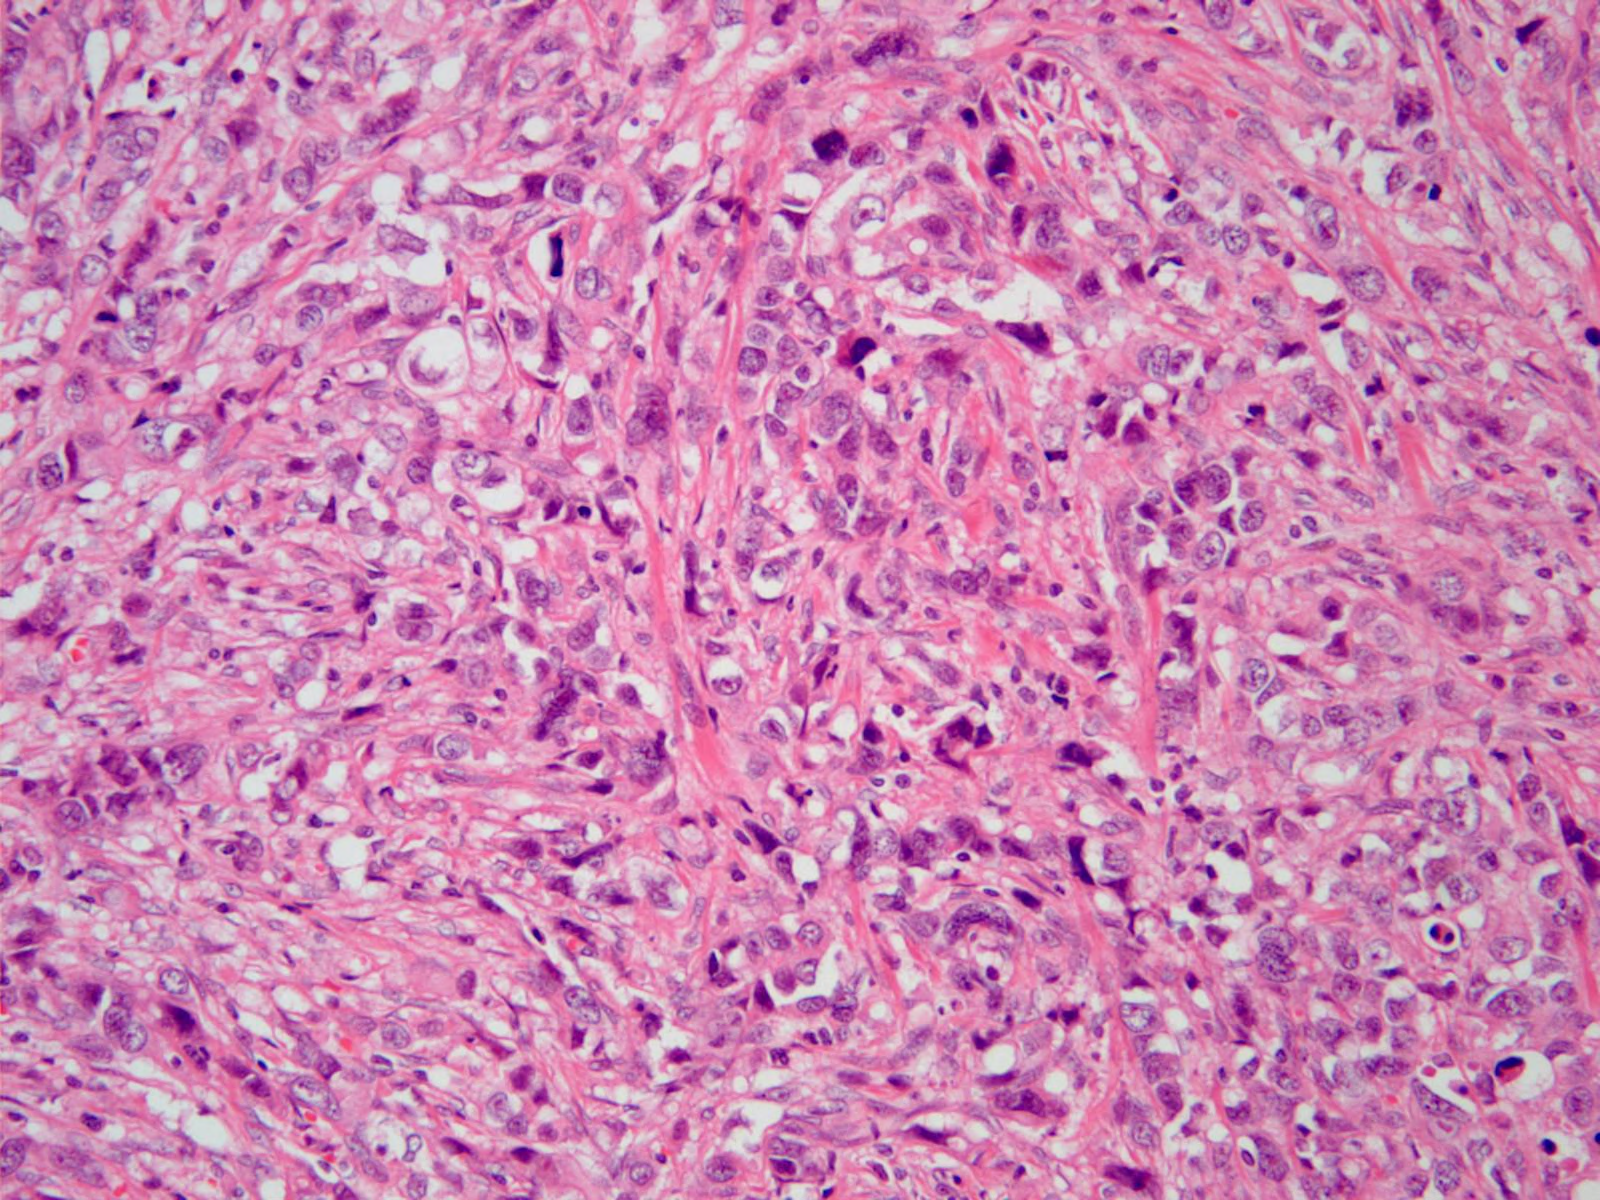
H&E image of one small field of the section — about 0.8 x 0.6 mm across, formalin-fixed paraffin-embedded (FFPE) diagnostic section, primary tumour sample from the stomach. Male patient; age at initial diagnosis 78 years. Histologic grade: G3 (poorly differentiated).
Diagnosis: Adenocarcinoma, NOS (gastric antrum). Lymph nodes positive (case pathology): 2 of 8 examined.